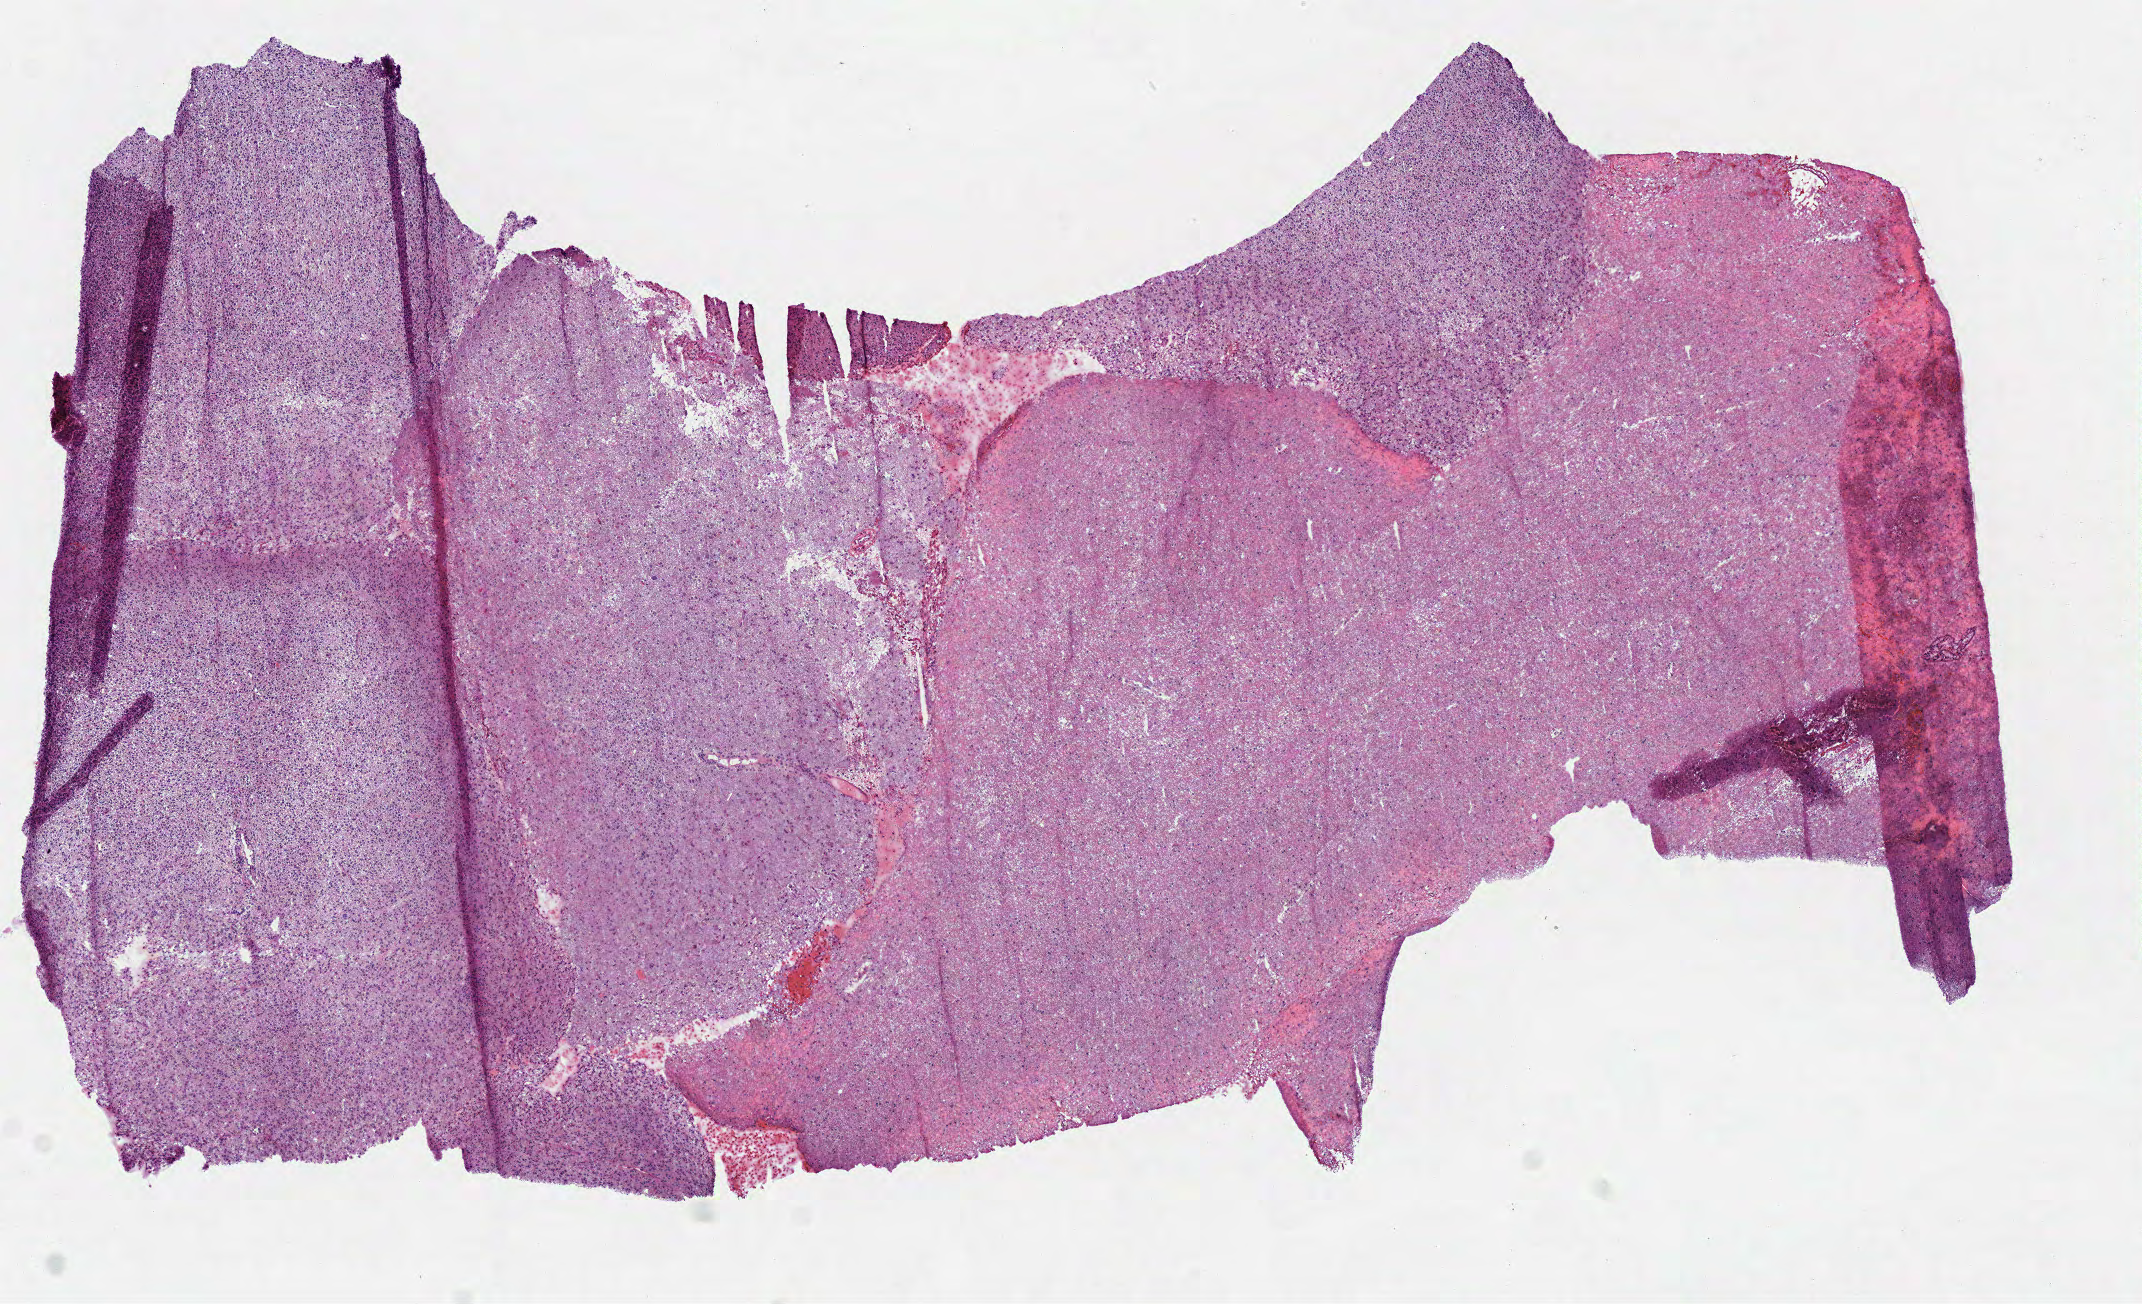
H&E whole-slide image, a low-resolution overview of the entire scanned area, about 8.4 x 5.1 mm, frozen section from the bottom of the tissue portion, primary tumour sample from the brain. Female patient; age at initial diagnosis 34 years.
Diagnosis: Astrocytoma, anaplastic.